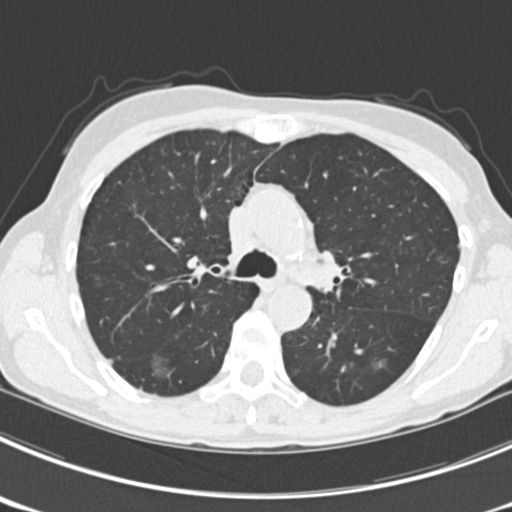
Axial slice from a low-dose chest CT screening exam, third screening round (two years after baseline), lung window (W 1500 / L -600 HU), standard (soft-tissue) reconstruction kernel (B30f), 120 kVp, slice 71 of 225 in the series, 512 × 512 image matrix. Female participant, aged 63 years at enrolment. Current smoker at enrolment.
2 expert reader's lesion annotations on this slice (largest first), box from (x=356, y=348) to (x=399, y=384) px; (x=143, y=347)–(x=181, y=386). The screening reader recorded 9 non-calcified nodules or masses ≥4 mm on this exam (left upper lobe, right upper lobe, left upper lobe, left lower lobe, right middle lobe, left lower lobe, left lower lobe, right lower lobe, right lower lobe); which of them these boxes mark is not recorded. Official screen result: positive, other.